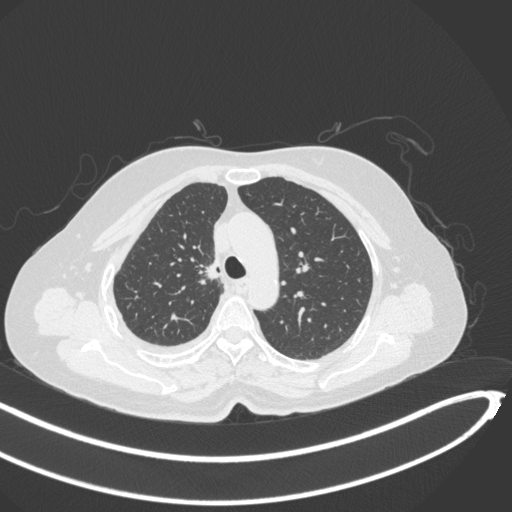
Chest CT, one axial slice; position 223 of 297 along the scan axis; reconstruction kernel B31f; 120 kVp; lung window (W 1500 / L -600 HU); 1 mm slice thickness; 512 × 512 image matrix, field of view 400 × 400 mm. Female patient, age 64 years. From the clinical record (not read from this slice): clinical TNM (as recorded): T1b N0 M1.
Structures marked on this image (rectangle marked by the reading radiologist):
- lung tumour (recorded histology: adenocarcinoma): bounding box [x1, y1, x2, y2] px = [198, 255, 220, 287]